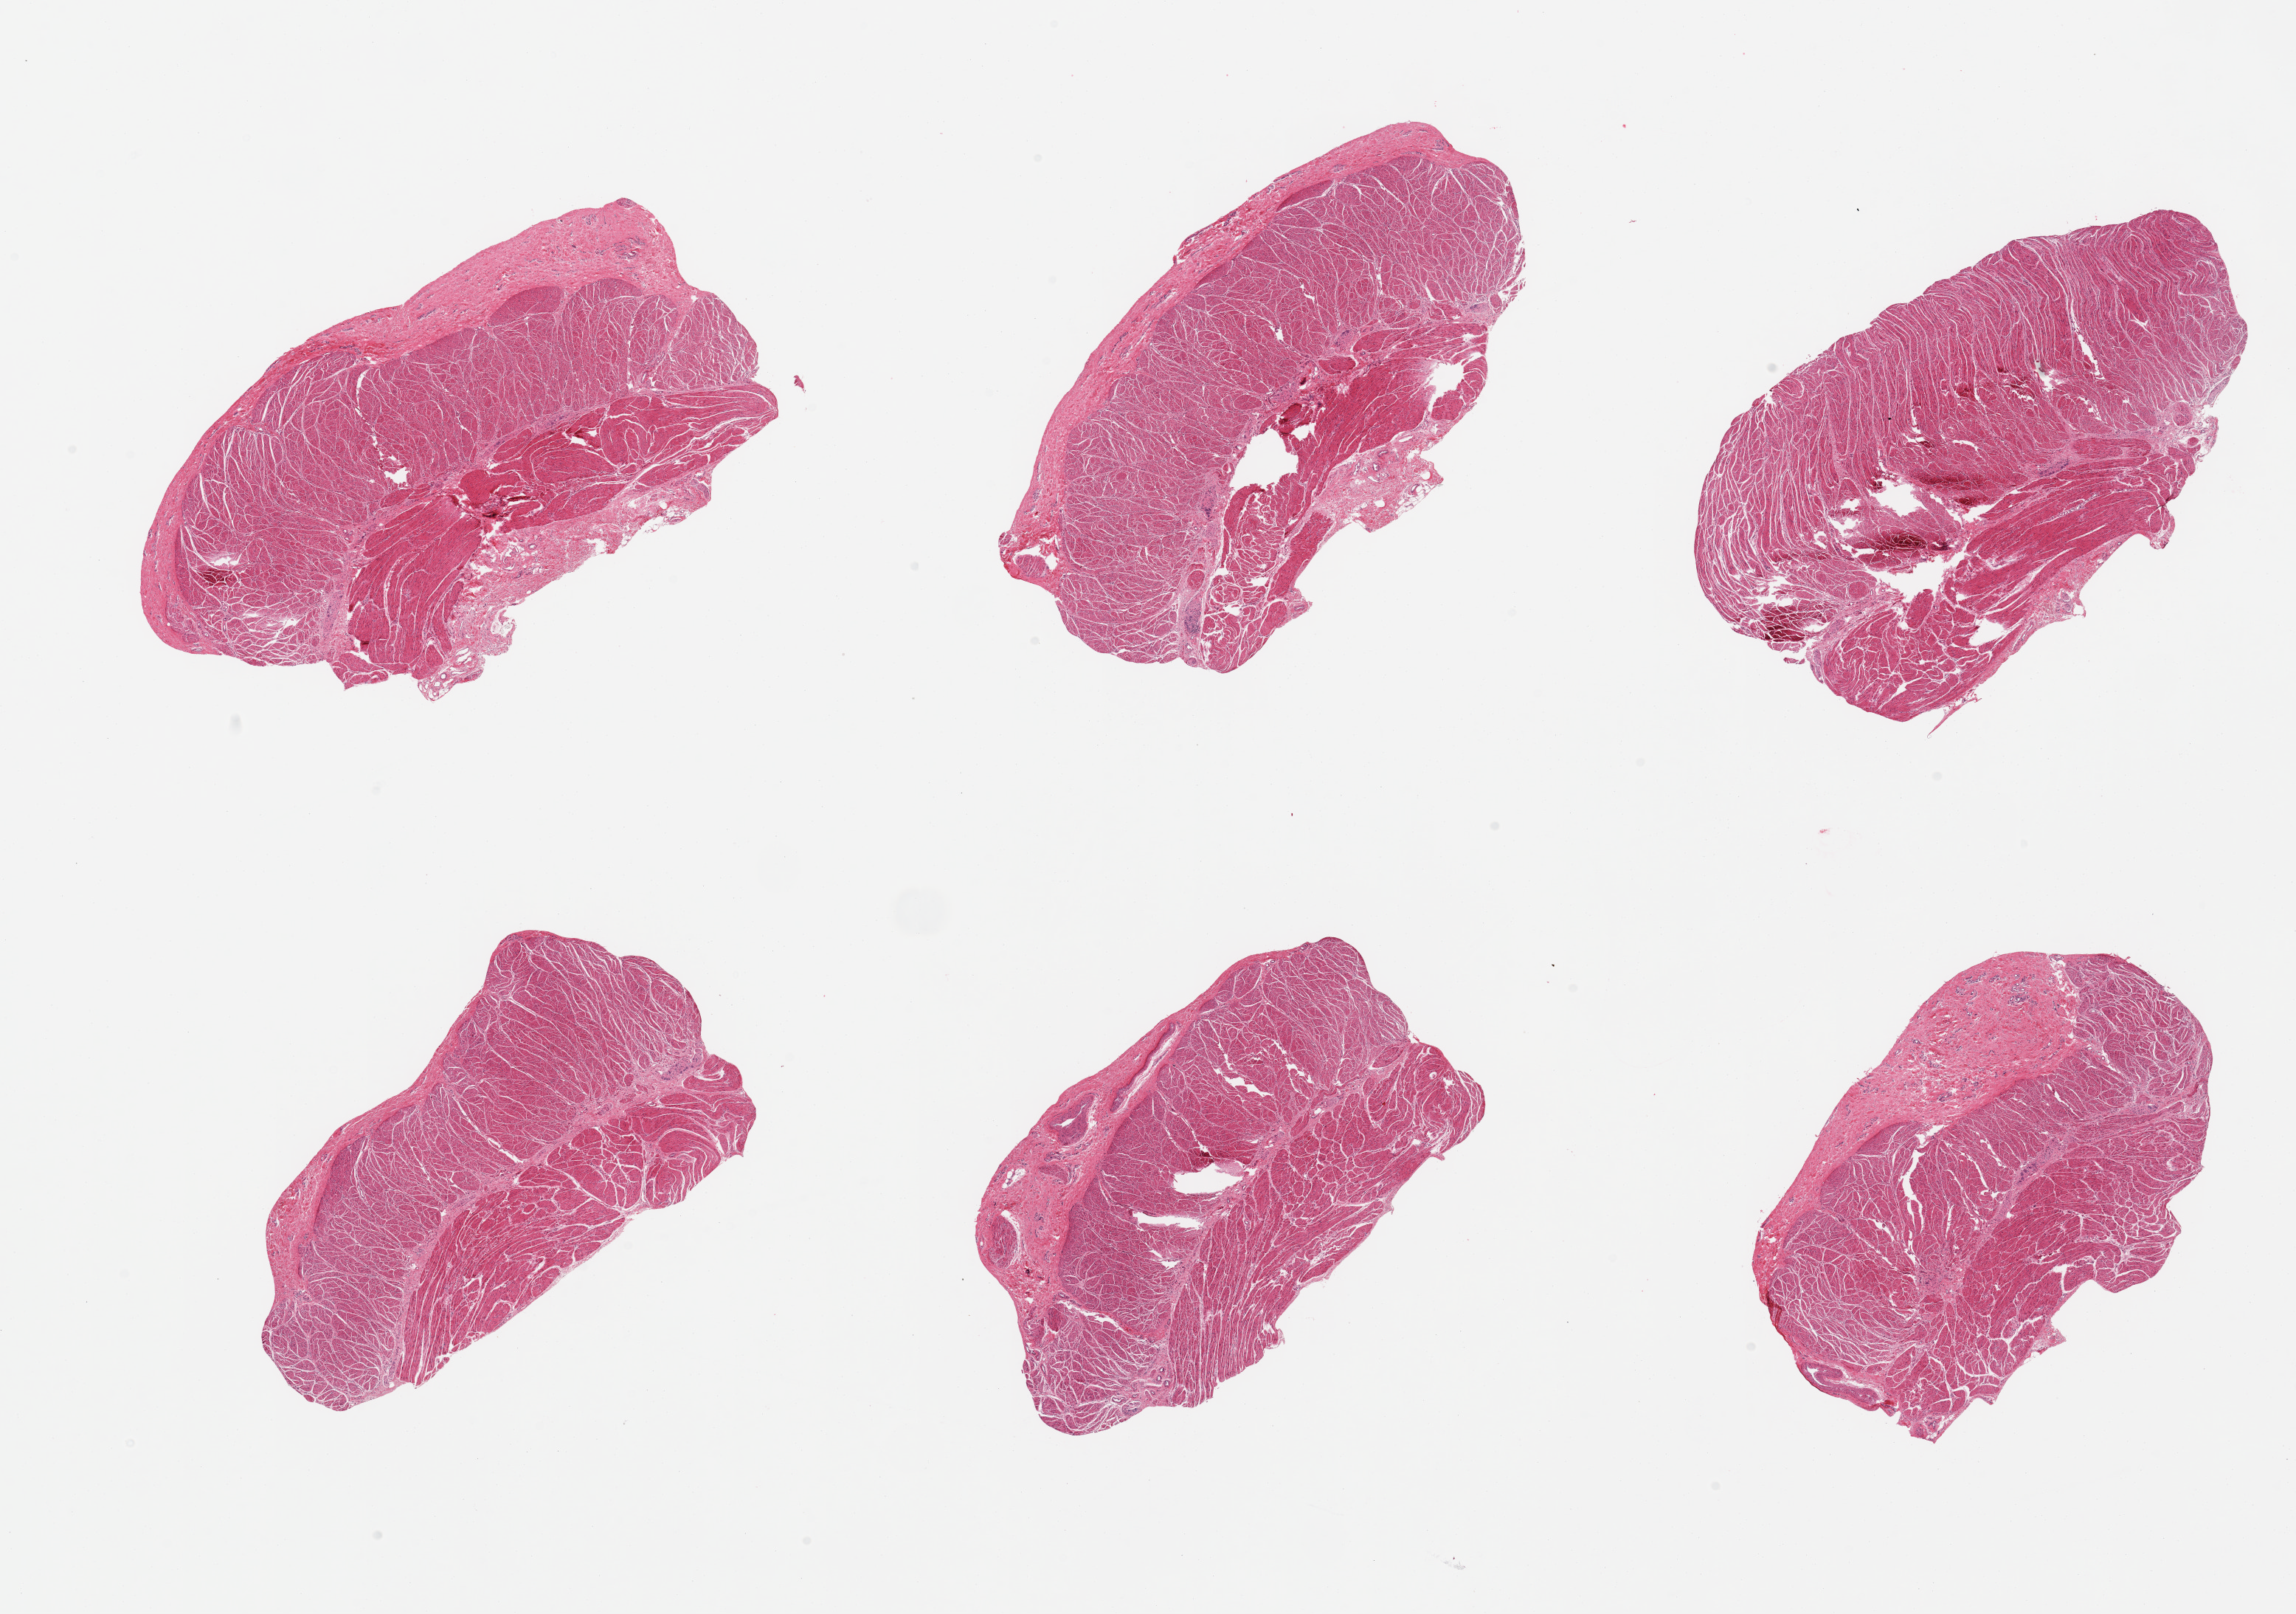
Digitized haematoxylin and eosin-stained section — shown as a low-resolution overview of the whole scanned area (about 24.6 x 17.3 mm, slide scanned at 20x). PAXgene-fixed, paraffin-embedded tissue. Section of gastroesophageal junction (target tissue). Tissue donor sample. Donor: female.
- reviewer comment on this tissue sample: 6 pieces; well trimmed